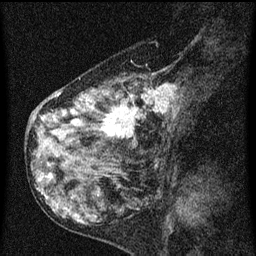
Breast MRI (dynamic contrast-enhanced), one sagittal slice. Dynamic contrast-enhanced series, image 2 of 3 at this slice position (ordered by acquisition). 1.5 T. TE 4.2 ms, TR 8 ms. 2 mm slice thickness. 256 × 256 image matrix, field of view 180 × 180 mm. Patient: female, 55 years.
Structures marked on this image (semi-automatic segmentation, software-assisted and operator-edited):
- analysis volume of interest (the breast-tissue region the enhancement analysis was run in; not a lesion): box from (x=42, y=72) to (x=185, y=155) px
- tumour enhancement mask (voxels above the 70 % enhancement threshold inside the analysis volume of interest): (x=56, y=84)–(x=178, y=139)